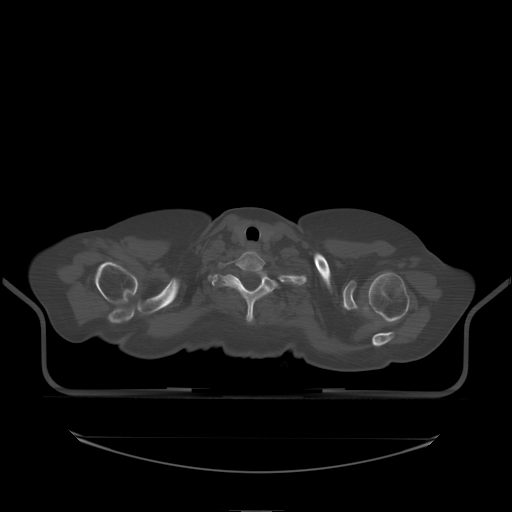
CT including the spine, one axial slice; slice 188 of 242 in the series (ordered by position); bone window (W 1800 / L 400 HU); 2.5 mm slice thickness; 512 × 512 image matrix, field of view 500 × 500 mm. Female patient, age 53 years. Case-level facts recorded for this patient, not image findings: primary cancer: lung; vertebrae with lytic lesions (as recorded): T7, L1.
Structures marked on this image (semi-automatic segmentation, software-assisted and operator-edited):
- T1 vertebra: bounding box [x1, y1, x2, y2] px = [214, 272, 279, 323]